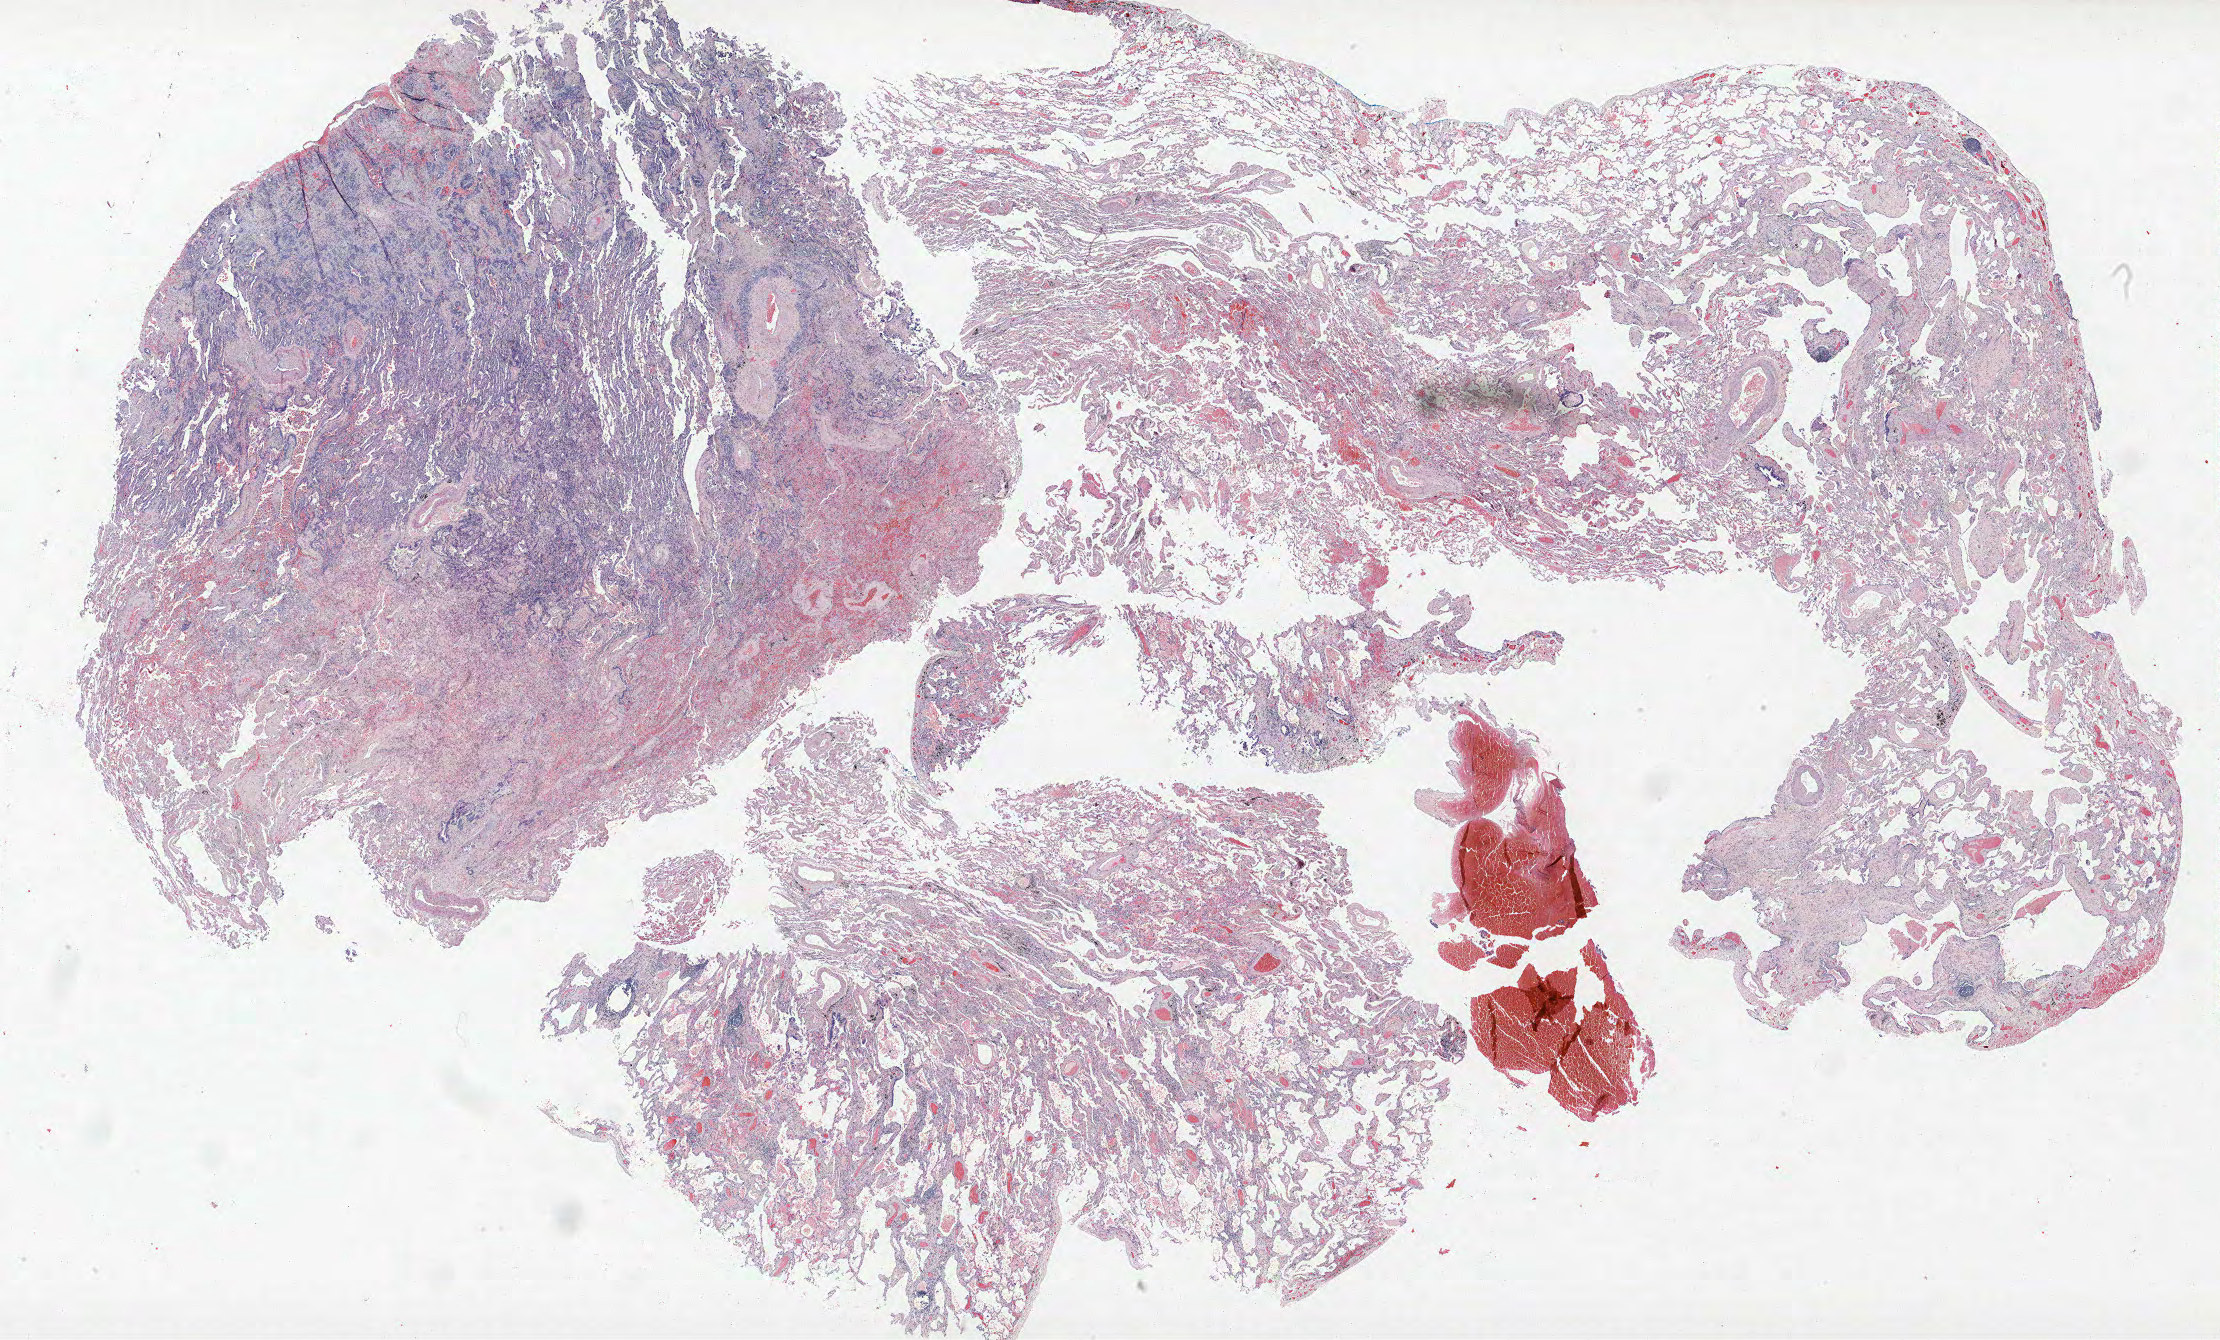
Whole-slide histology image, H&E, low-resolution overview of the scanned area, about 35.5 x 21.4 mm, FFPE section, lung. Male patient, aged 67 at enrolment. Grade: moderately differentiated (G2).
Stage (AJCC 6th edition): IB. Primary tumour location (clinical record): left upper lobe. Participant's lung-cancer diagnosis: Adenocarcinoma, NOS. Tumour size (pathology): 40 mm.